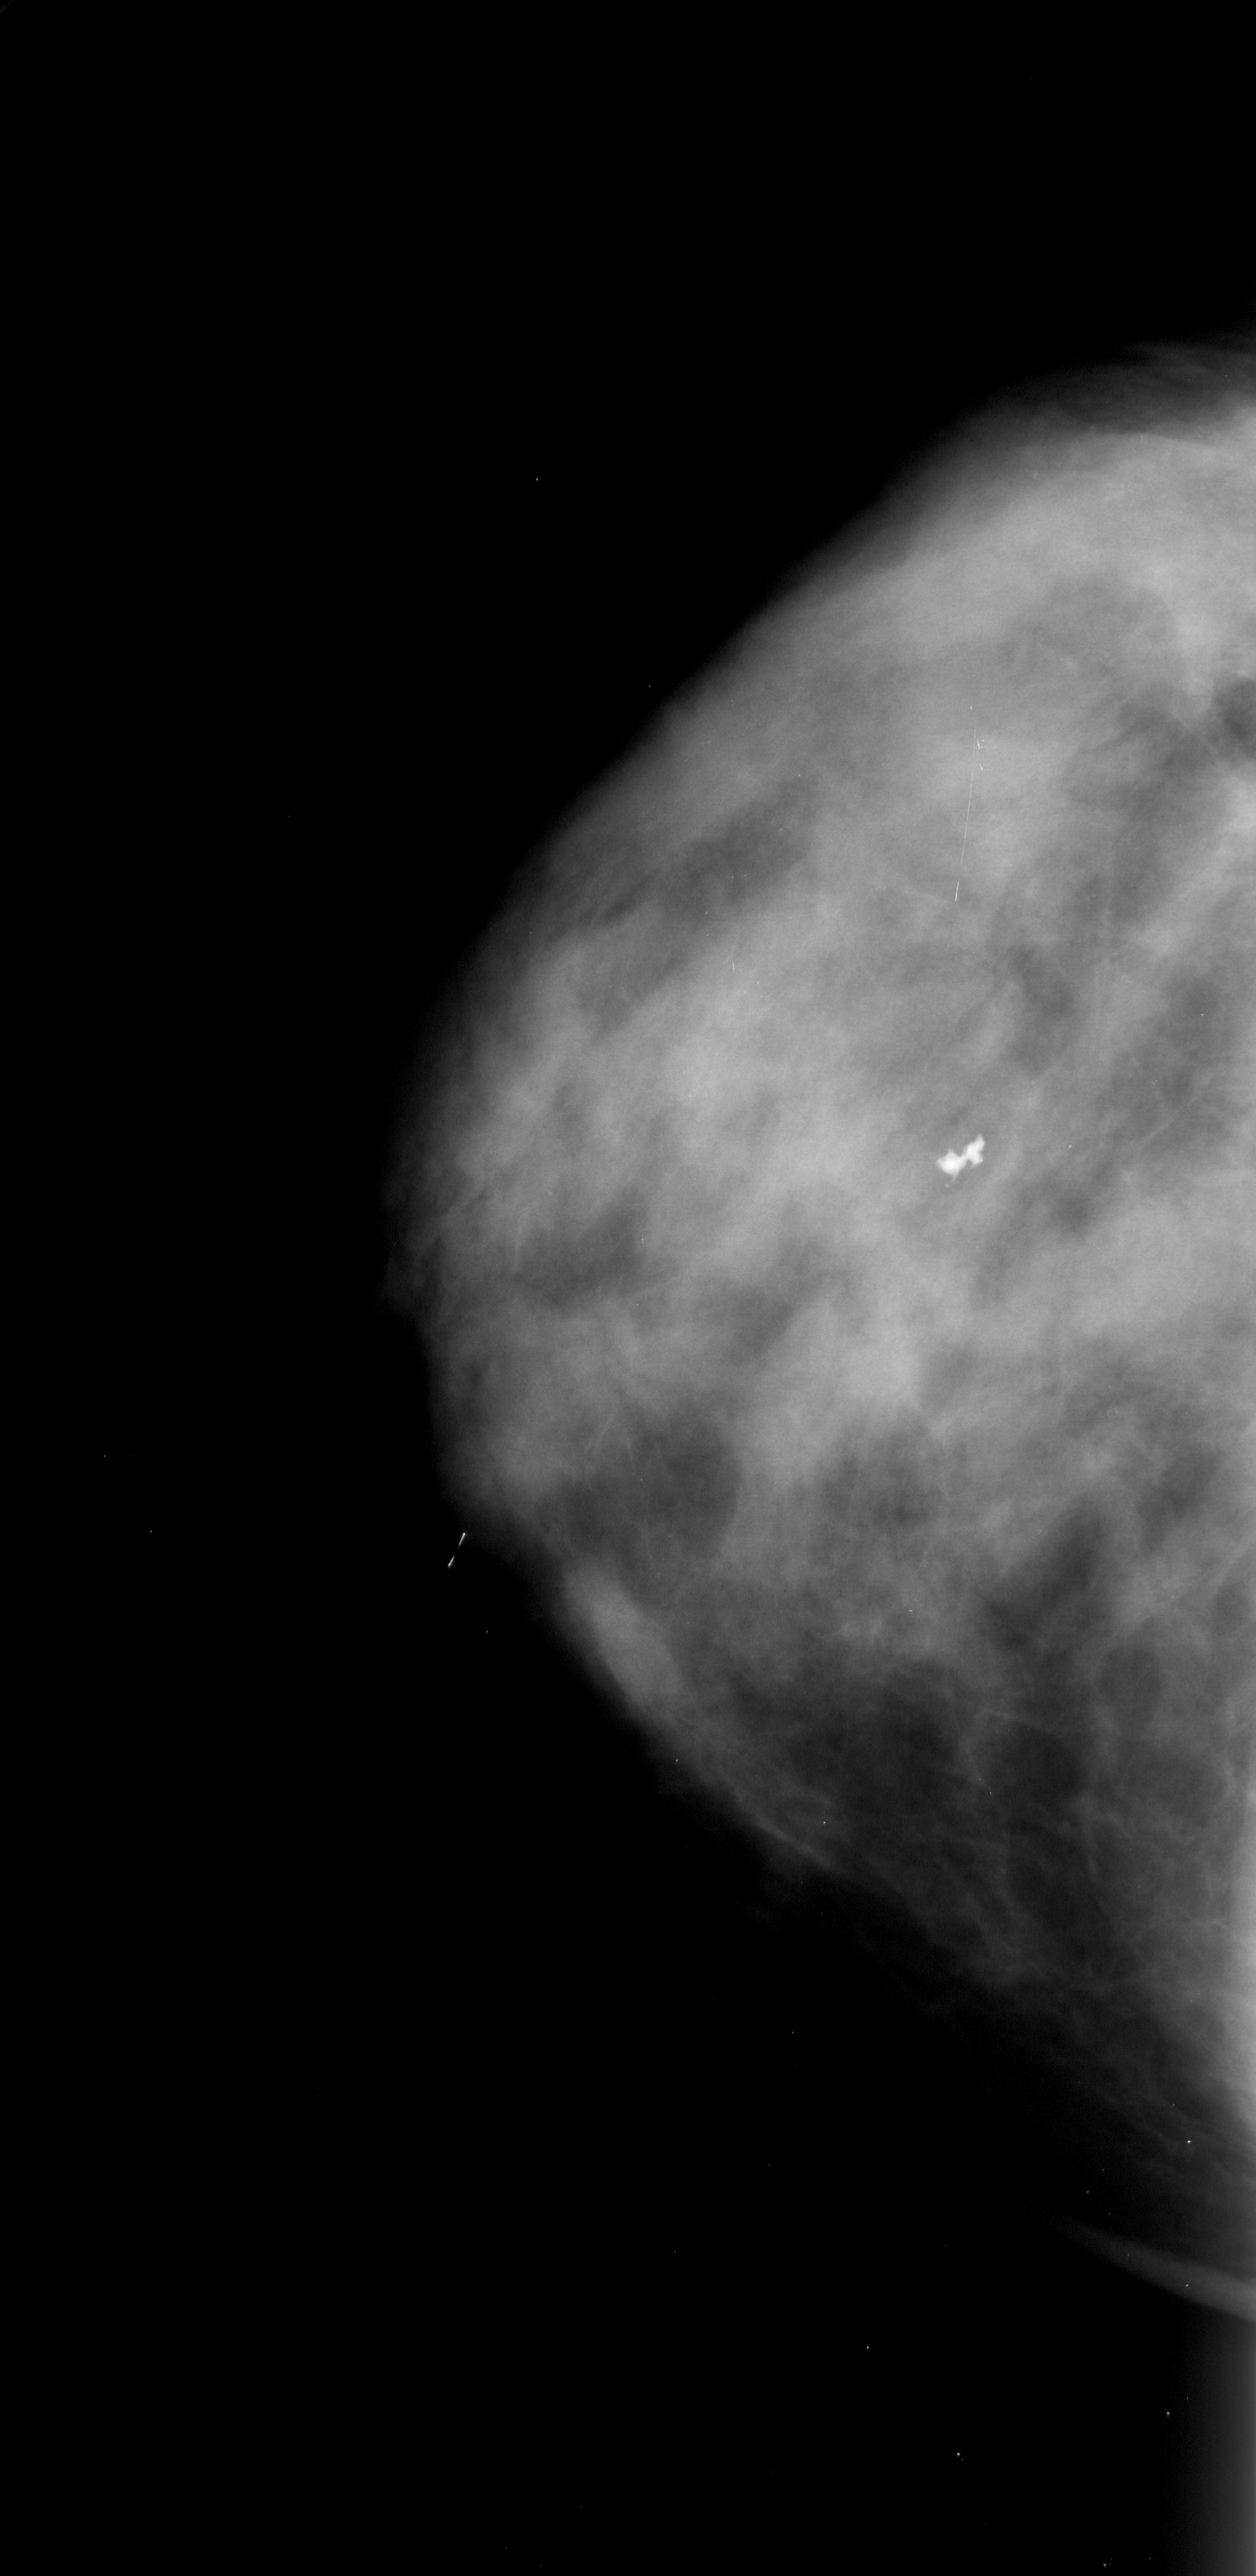
Digitized screen-film mammogram, left breast, CC view, breast composition: extremely dense (BI-RADS density category 4 of 4).
- Radiologist-marked abnormalities on this image: calcifications, morphology pleomorphic, distribution clustered; BI-RADS assessment category 4; pathology result (as recorded, not read from the image): malignant.